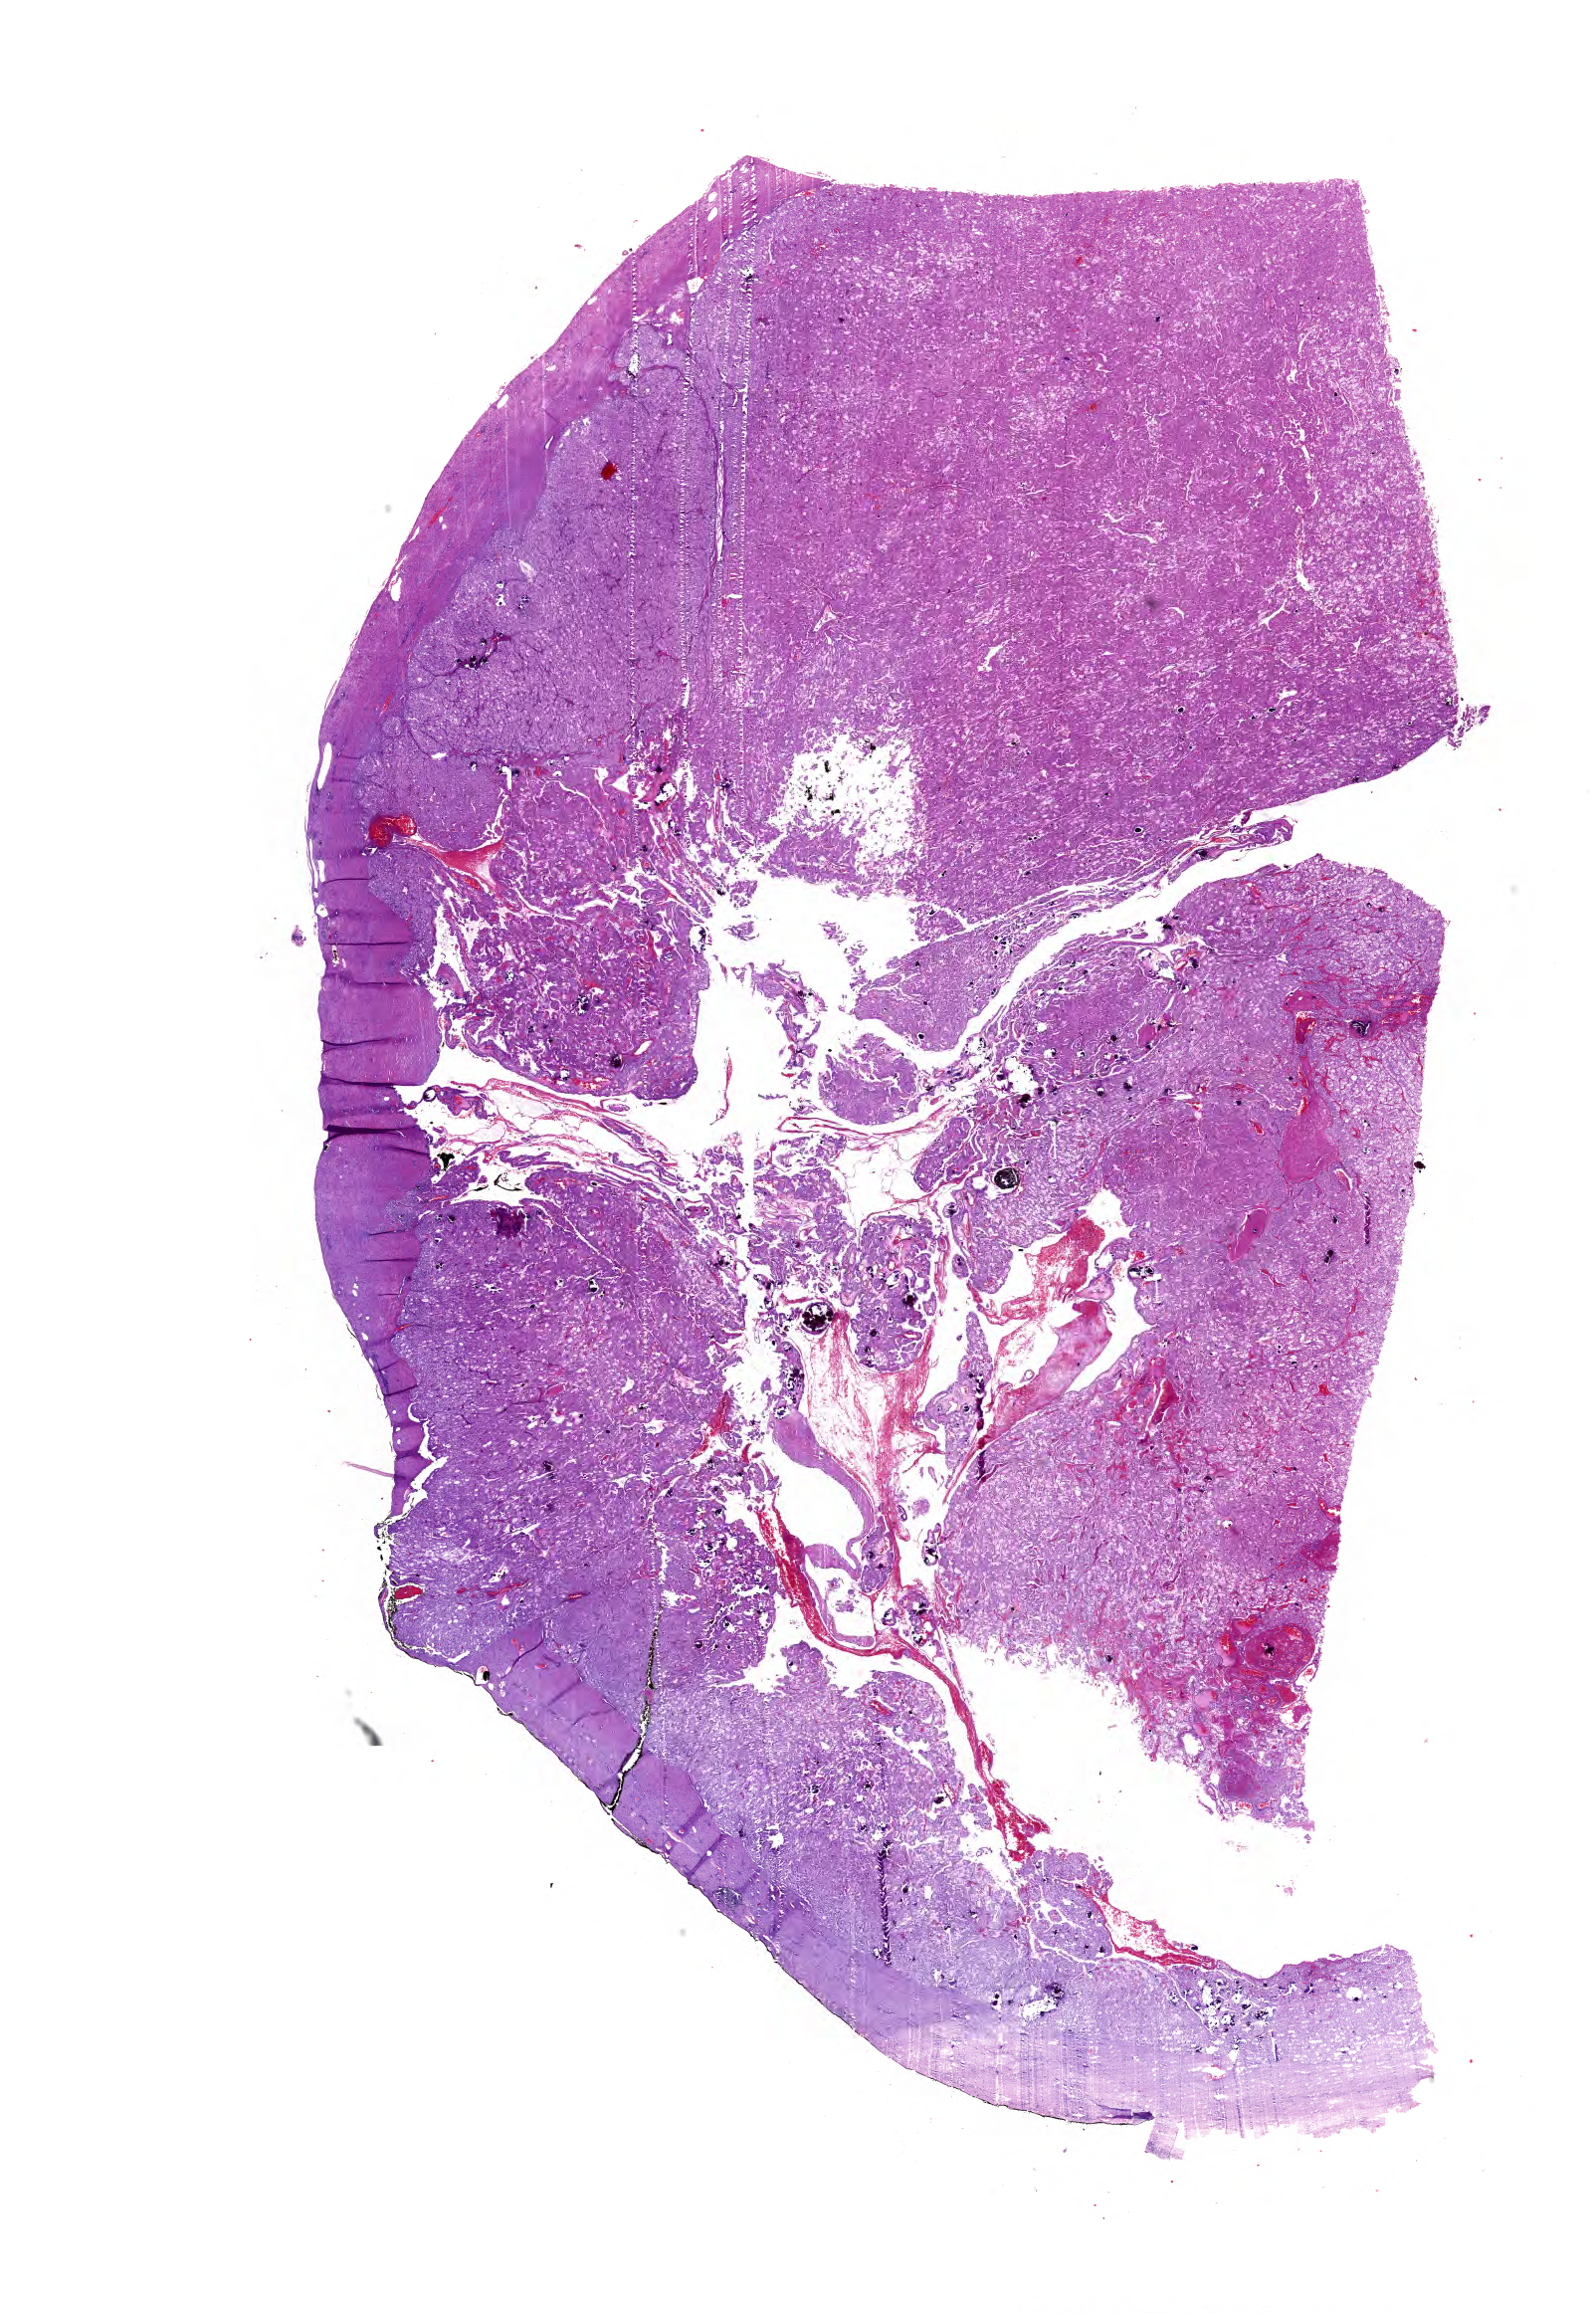
Digitized H&E tissue section (whole slide) — whole scanned area (about 20.0 x 28.9 mm, acquisition: 40x scan) shown as a low-resolution overview; FFPE section; kidney, primary tumour sample. Male patient; age at initial diagnosis 77 years.
• pathologic diagnosis: Papillary adenocarcinoma, NOS
• laterality: right